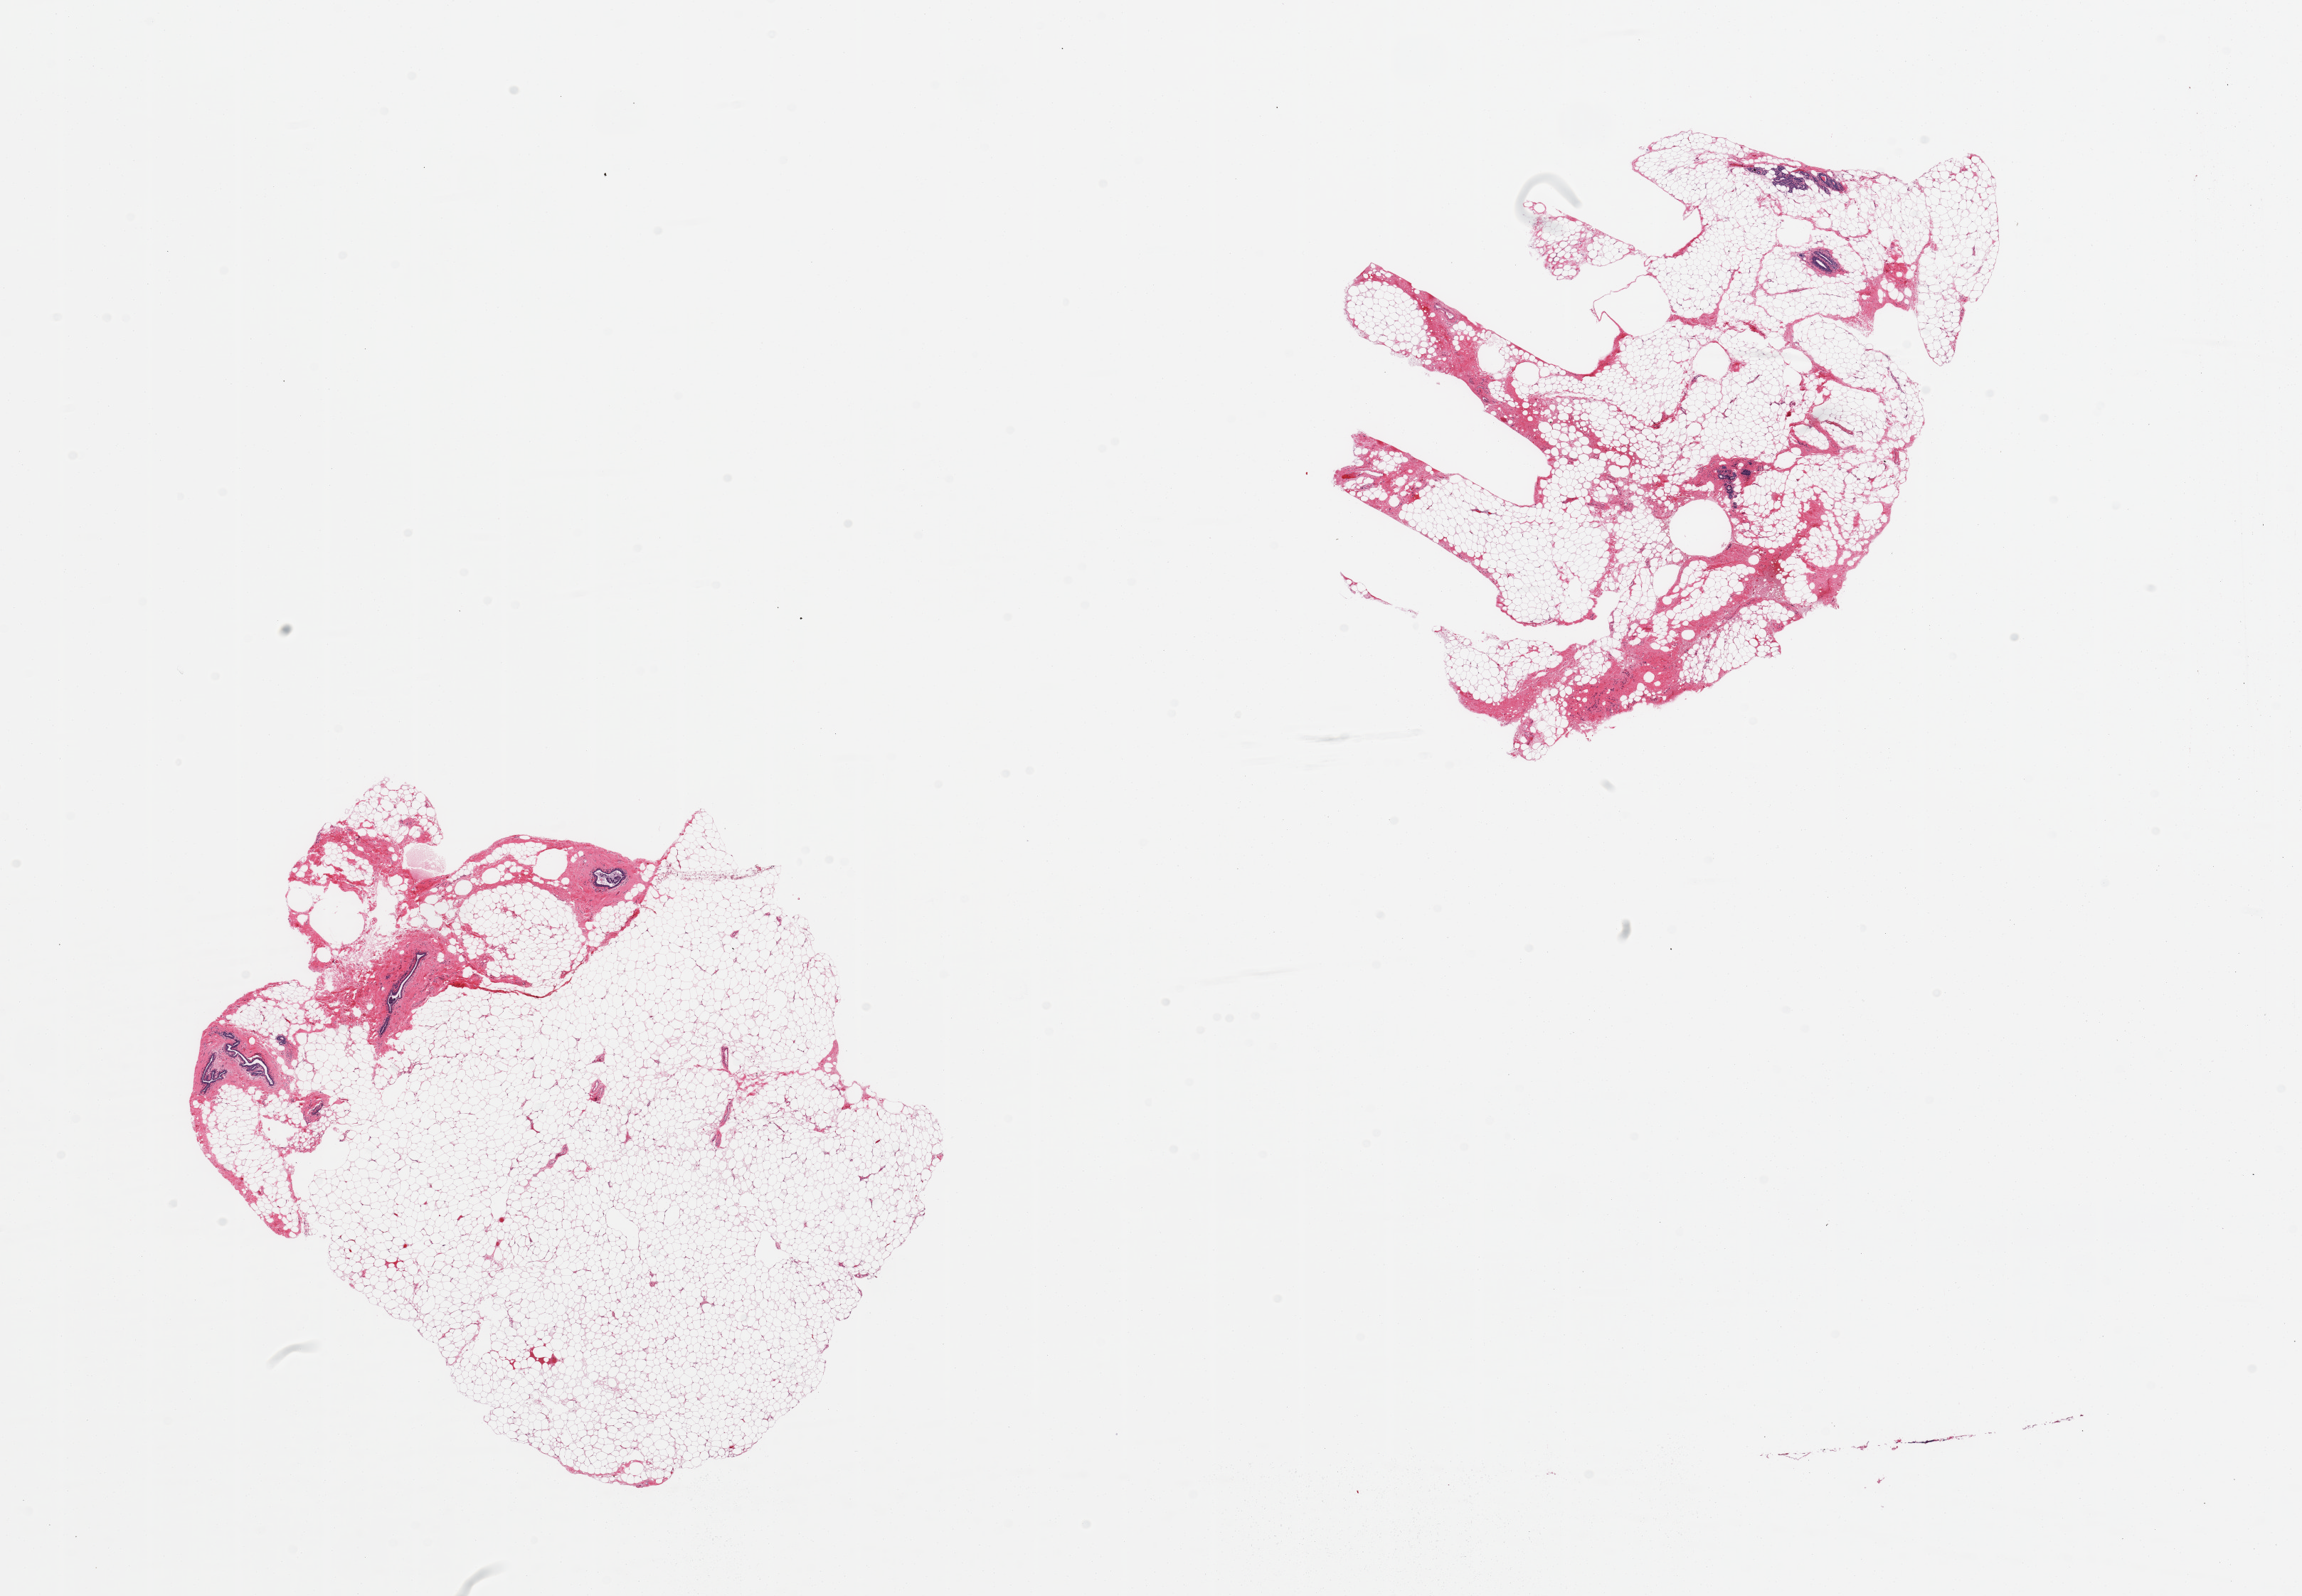
Digitized H&E-stained section, brightfield — low-resolution overview of the scanned area, about 25.6 x 17.7 mm (acquisition: 20x scan); PAXgene-fixed, paraffin-embedded tissue; section of breast (target tissue); tissue donor sample. Female donor.
- pathologist's review note for this sample: 2 pieces; 80-90% adipose tissue with small contribution of fibrous stroma and ducts/few lobules